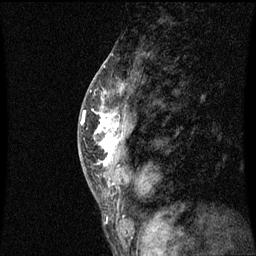
Breast MRI (dynamic contrast-enhanced), one sagittal slice. Slice 35 of 60 in the series (ordered by position). Dynamic contrast-enhanced series, image 2 of 3 at this slice position (ordered by acquisition). 1.5 T. TE 4.2 ms, TR 8.9 ms. 2 mm slice thickness. 256 × 256 image matrix, field of view 200 × 200 mm. Female patient, age 50 years. Case-level facts recorded for this patient, not image findings: setting: breast cancer imaged before/during neoadjuvant chemotherapy; receptor status: triple-negative.
Annotated regions visible in this slice (semi-automatically segmented with operator editing):
- analysis volume of interest (the breast-tissue region the enhancement analysis was run in; not a lesion): box from (x=84, y=80) to (x=135, y=171) px
- tumour enhancement mask (voxels above the 70 % enhancement threshold inside the analysis volume of interest): (x=84, y=106)–(x=119, y=167)